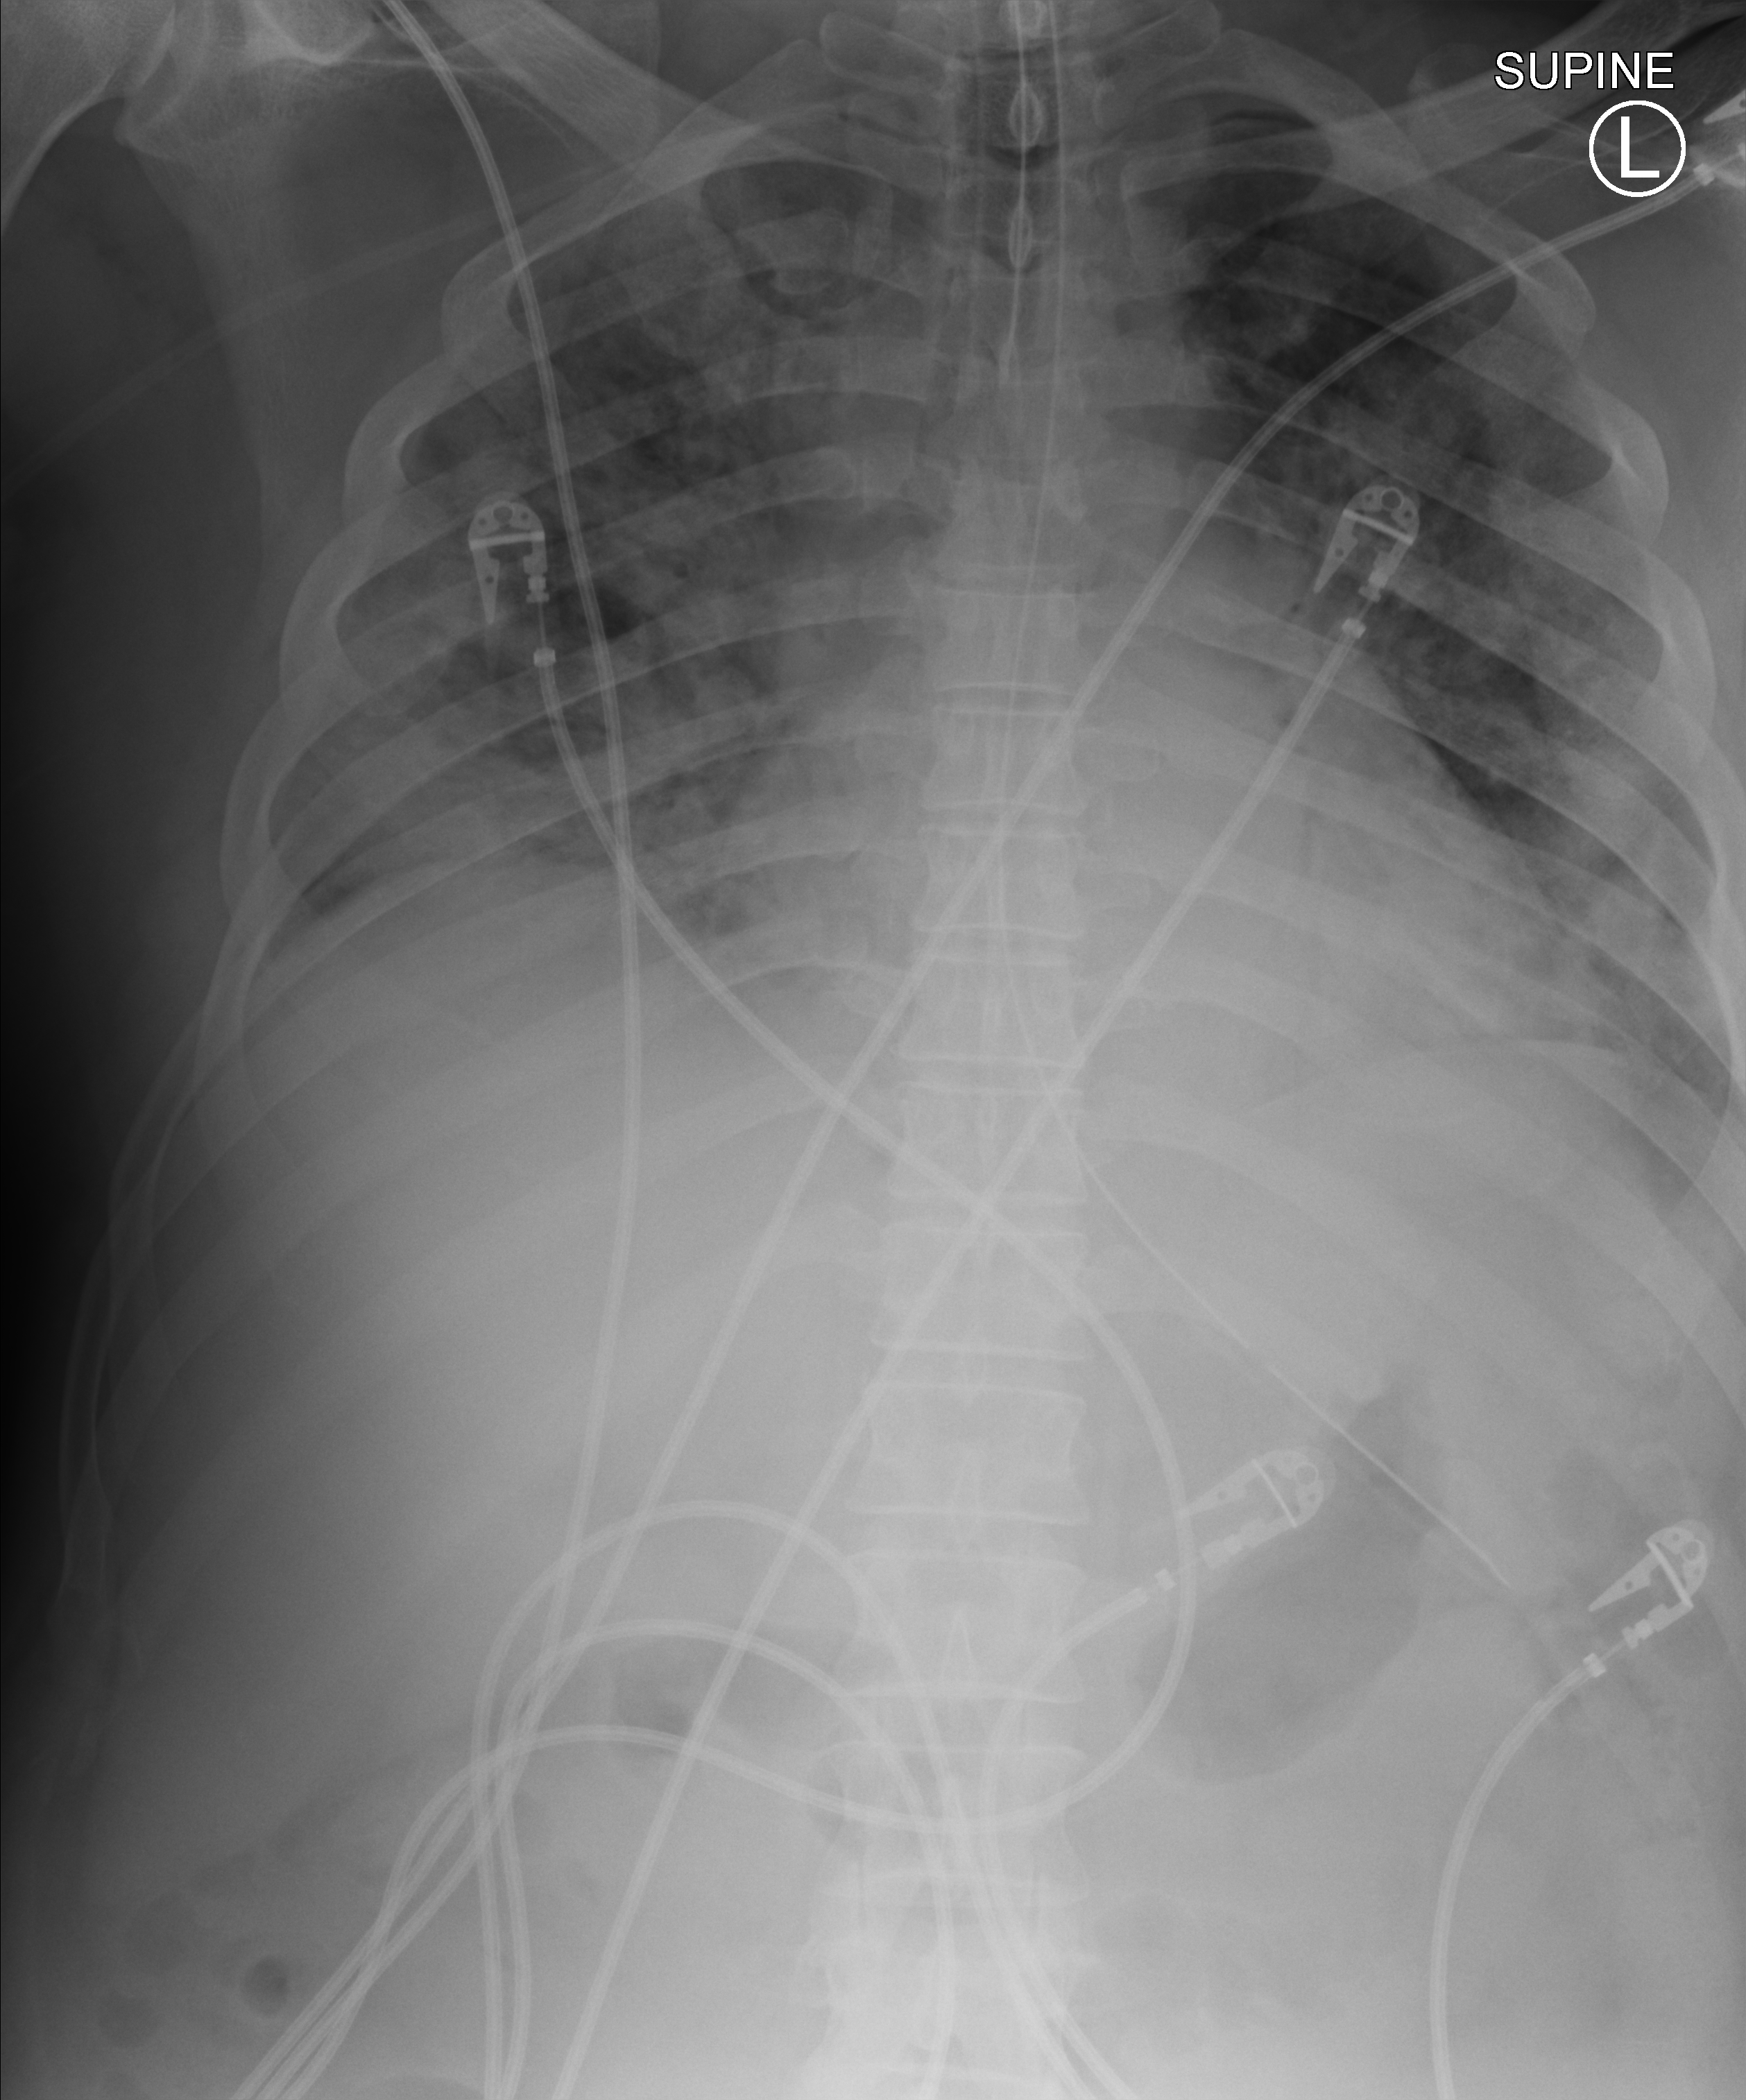
Bedside chest radiograph (computed radiography); anteroposterior (AP) projection. Male patient hospitalised with COVID-19, age 18–59 years.
Admission-level facts for this patient (not findings on this image; timing relative to this image not recorded):
- hypertension (admission record): no
- admitted to intensive care during this hospital stay: yes